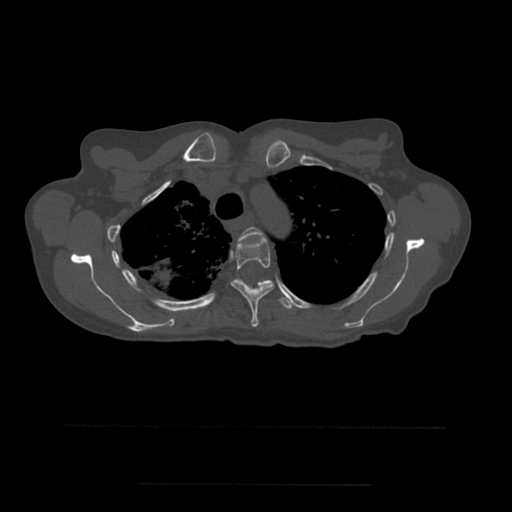
CT including the spine, one axial slice; position 406 of 544 along the scan axis; bone window (W 1800 / L 400 HU); 512 × 512 image matrix, field of view 350 × 350 mm. Patient age 58 years. Case-level facts recorded for this patient, not image findings: primary cancer: lung.
Annotated regions visible in this slice (semi-automatically segmented with operator editing):
- T3 vertebra: box from (x=238, y=227) to (x=267, y=243) px
- T4 vertebra: (x=231, y=237)–(x=274, y=327)
- T5 vertebra: (x=235, y=279)–(x=295, y=310)